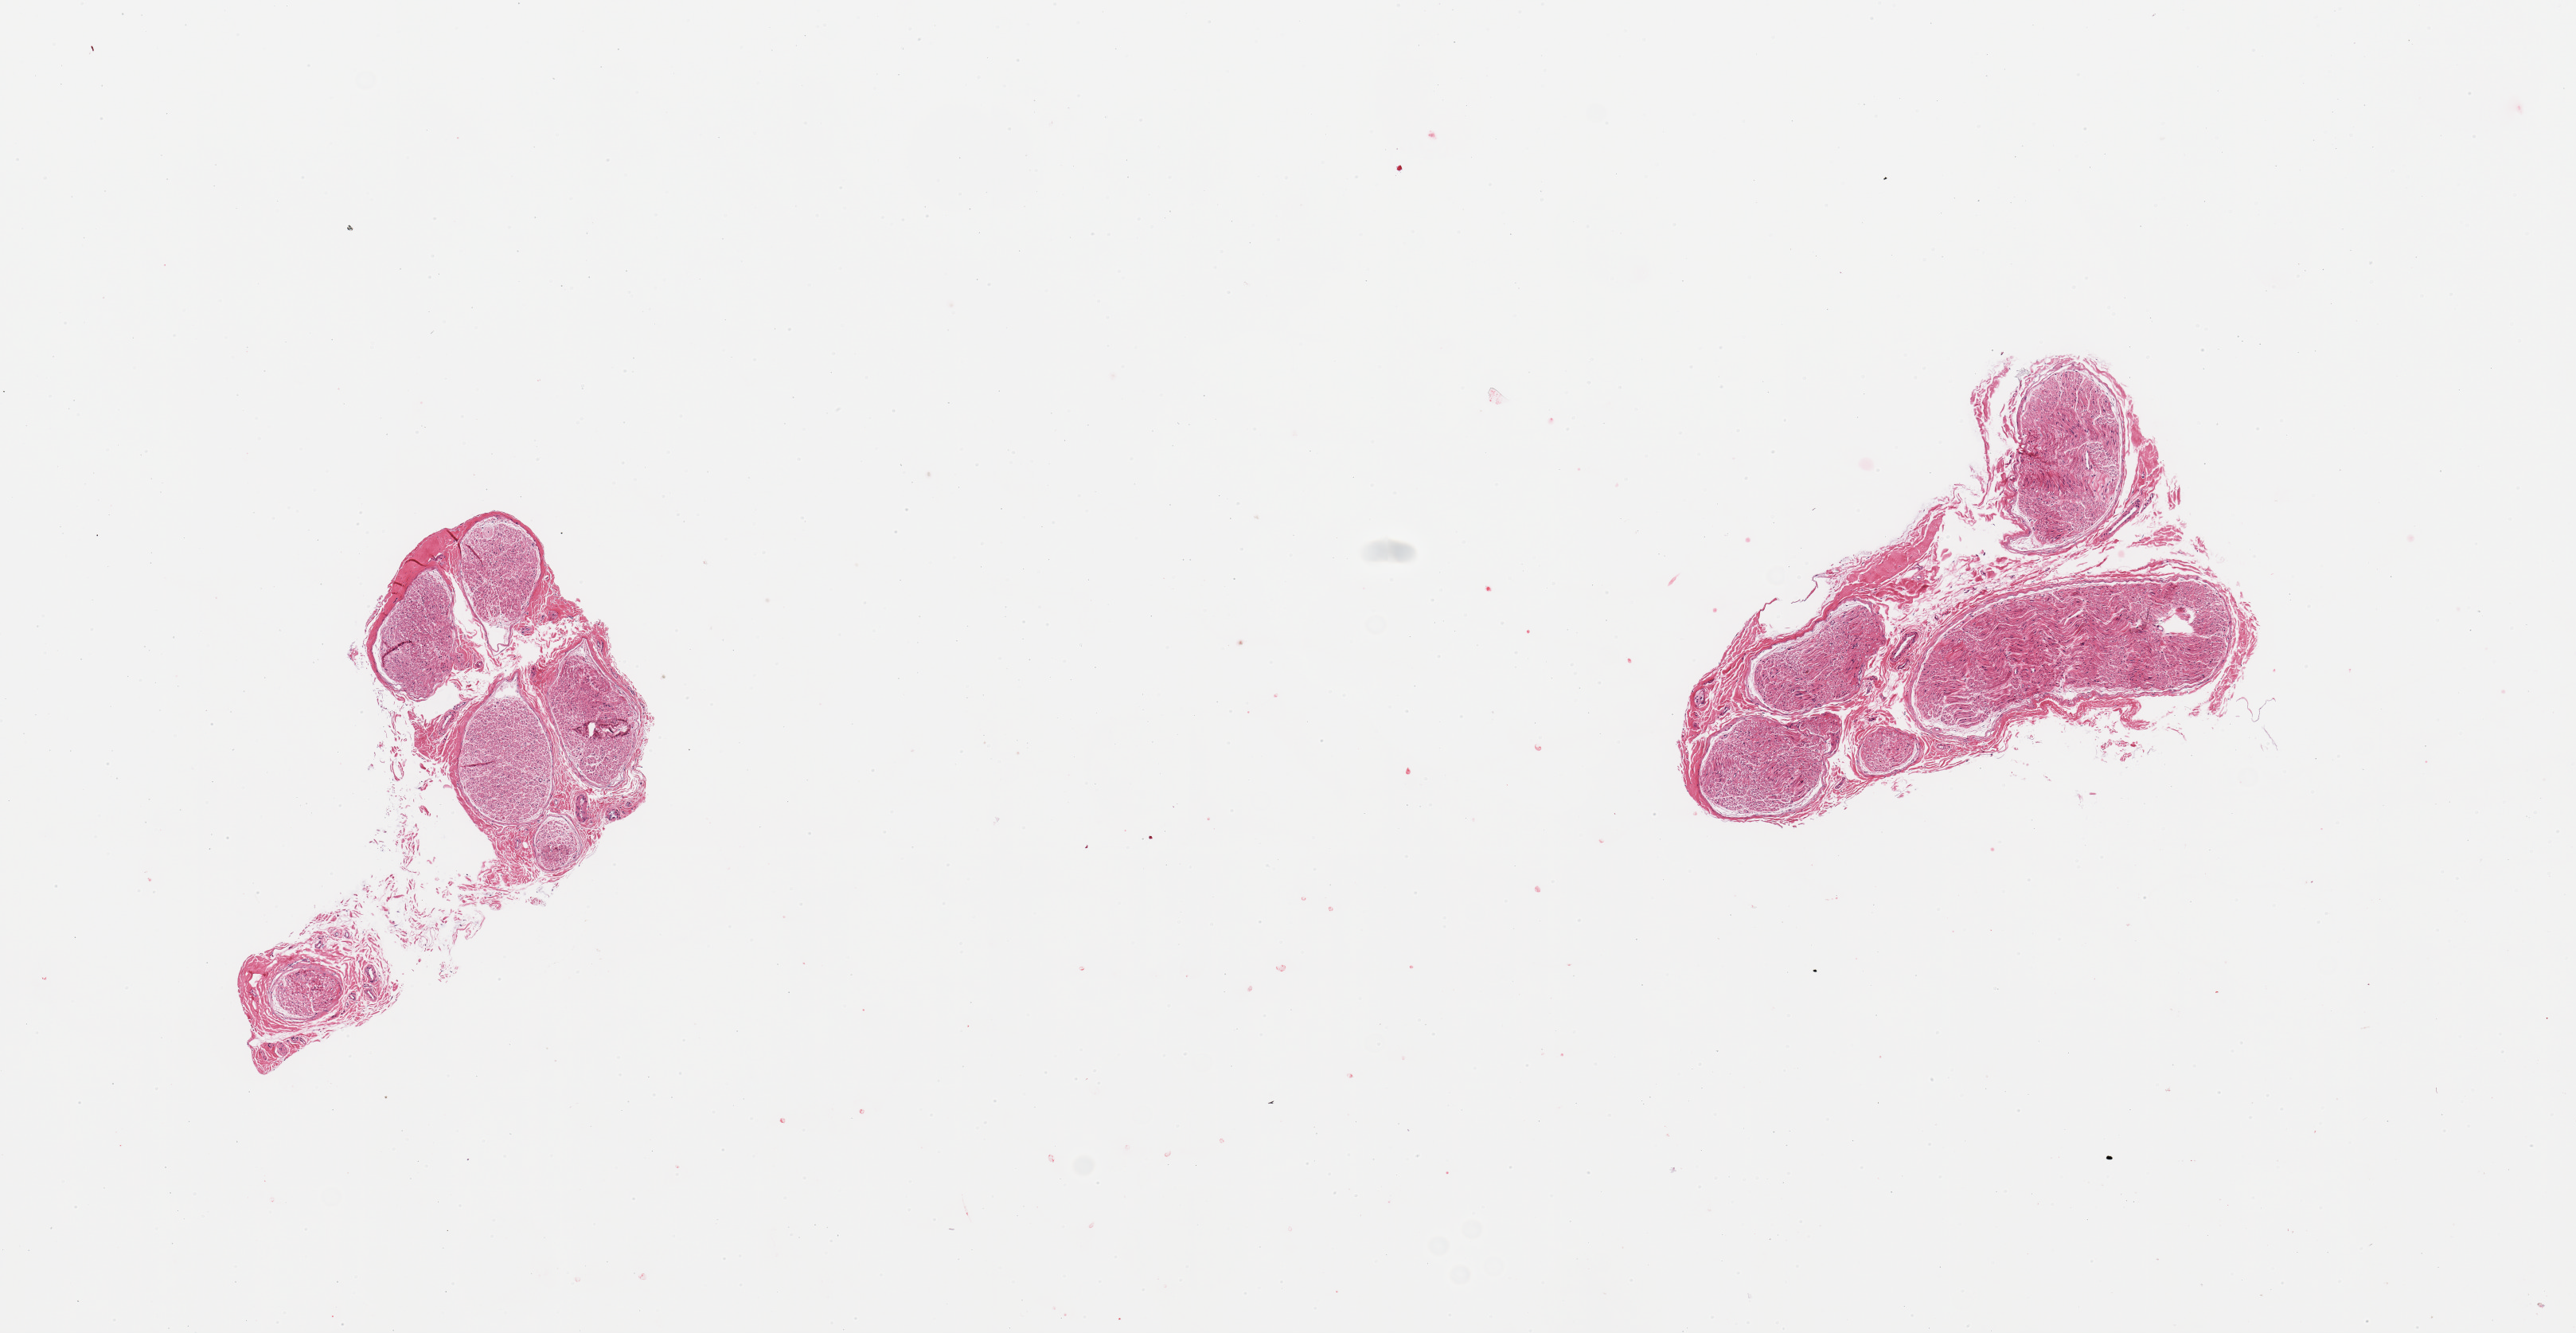
H&E whole-slide image, brightfield — whole scanned area (about 12.8 x 6.6 mm, from a 20x scan) shown as a low-resolution overview, PAXgene-fixed paraffin-embedded (PFPE) section, sampled site (target tissue): tibial nerve, donor tissue sample. Donor: male.
Review note (as recorded): 2 pieces.